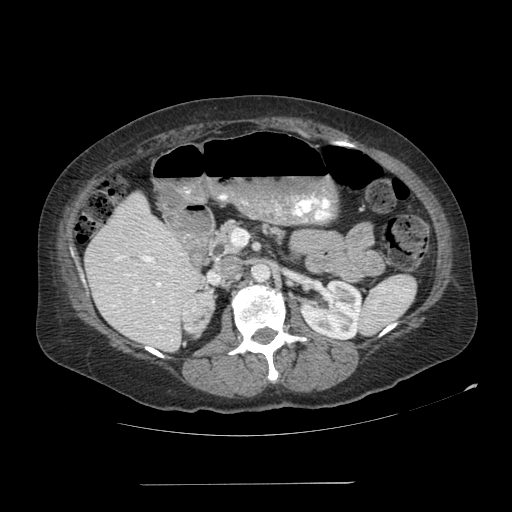
Contrast-enhanced abdominal CT, one axial slice; slice 52 of 113 in the series (ordered by position); 120 kVp; soft-tissue window (W 400 / L 40 HU); 512 × 512 image matrix. Female patient, age 67 years. From the clinical record (not read from this slice): diagnosis: adrenocortical carcinoma; tumour side: right adrenal; tumour size at pathology: 9.8 cm; Ki-67 index: 59 %; stage (as recorded): 4.
Outlined on this slice (semi-automatically segmented with operator editing):
- mass: bounding box [x1, y1, x2, y2] px = [184, 294, 214, 334]